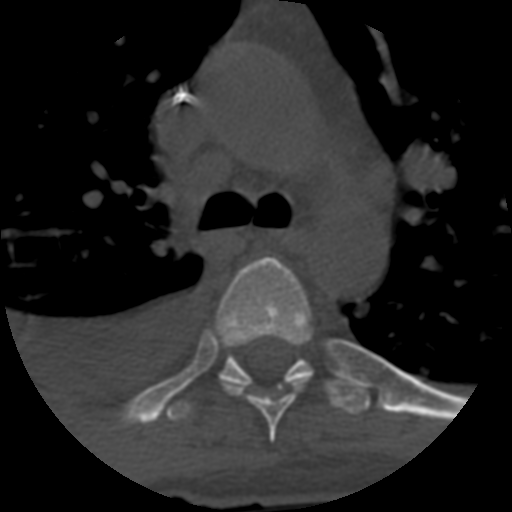
CT including the spine, one axial slice. Slice 446 of 708 in the series (ordered by position). 120 kVp. One of 3 acquisitions stored at this slice position. Bone window (W 1800 / L 400 HU). 1.25 mm slice thickness. 512 × 512 image matrix. Patient age 55 years. Case-level facts recorded for this patient, not image findings: primary cancer: colon; vertebrae with lytic lesions (as recorded): T12, L1, L5.
Outlined on this slice (semi-automatic segmentation, software-assisted and operator-edited):
- T5 vertebra: bounding box <216,256,311,442> (left, top, right, bottom; pixels)
- T6 vertebra: <164,353,371,422>